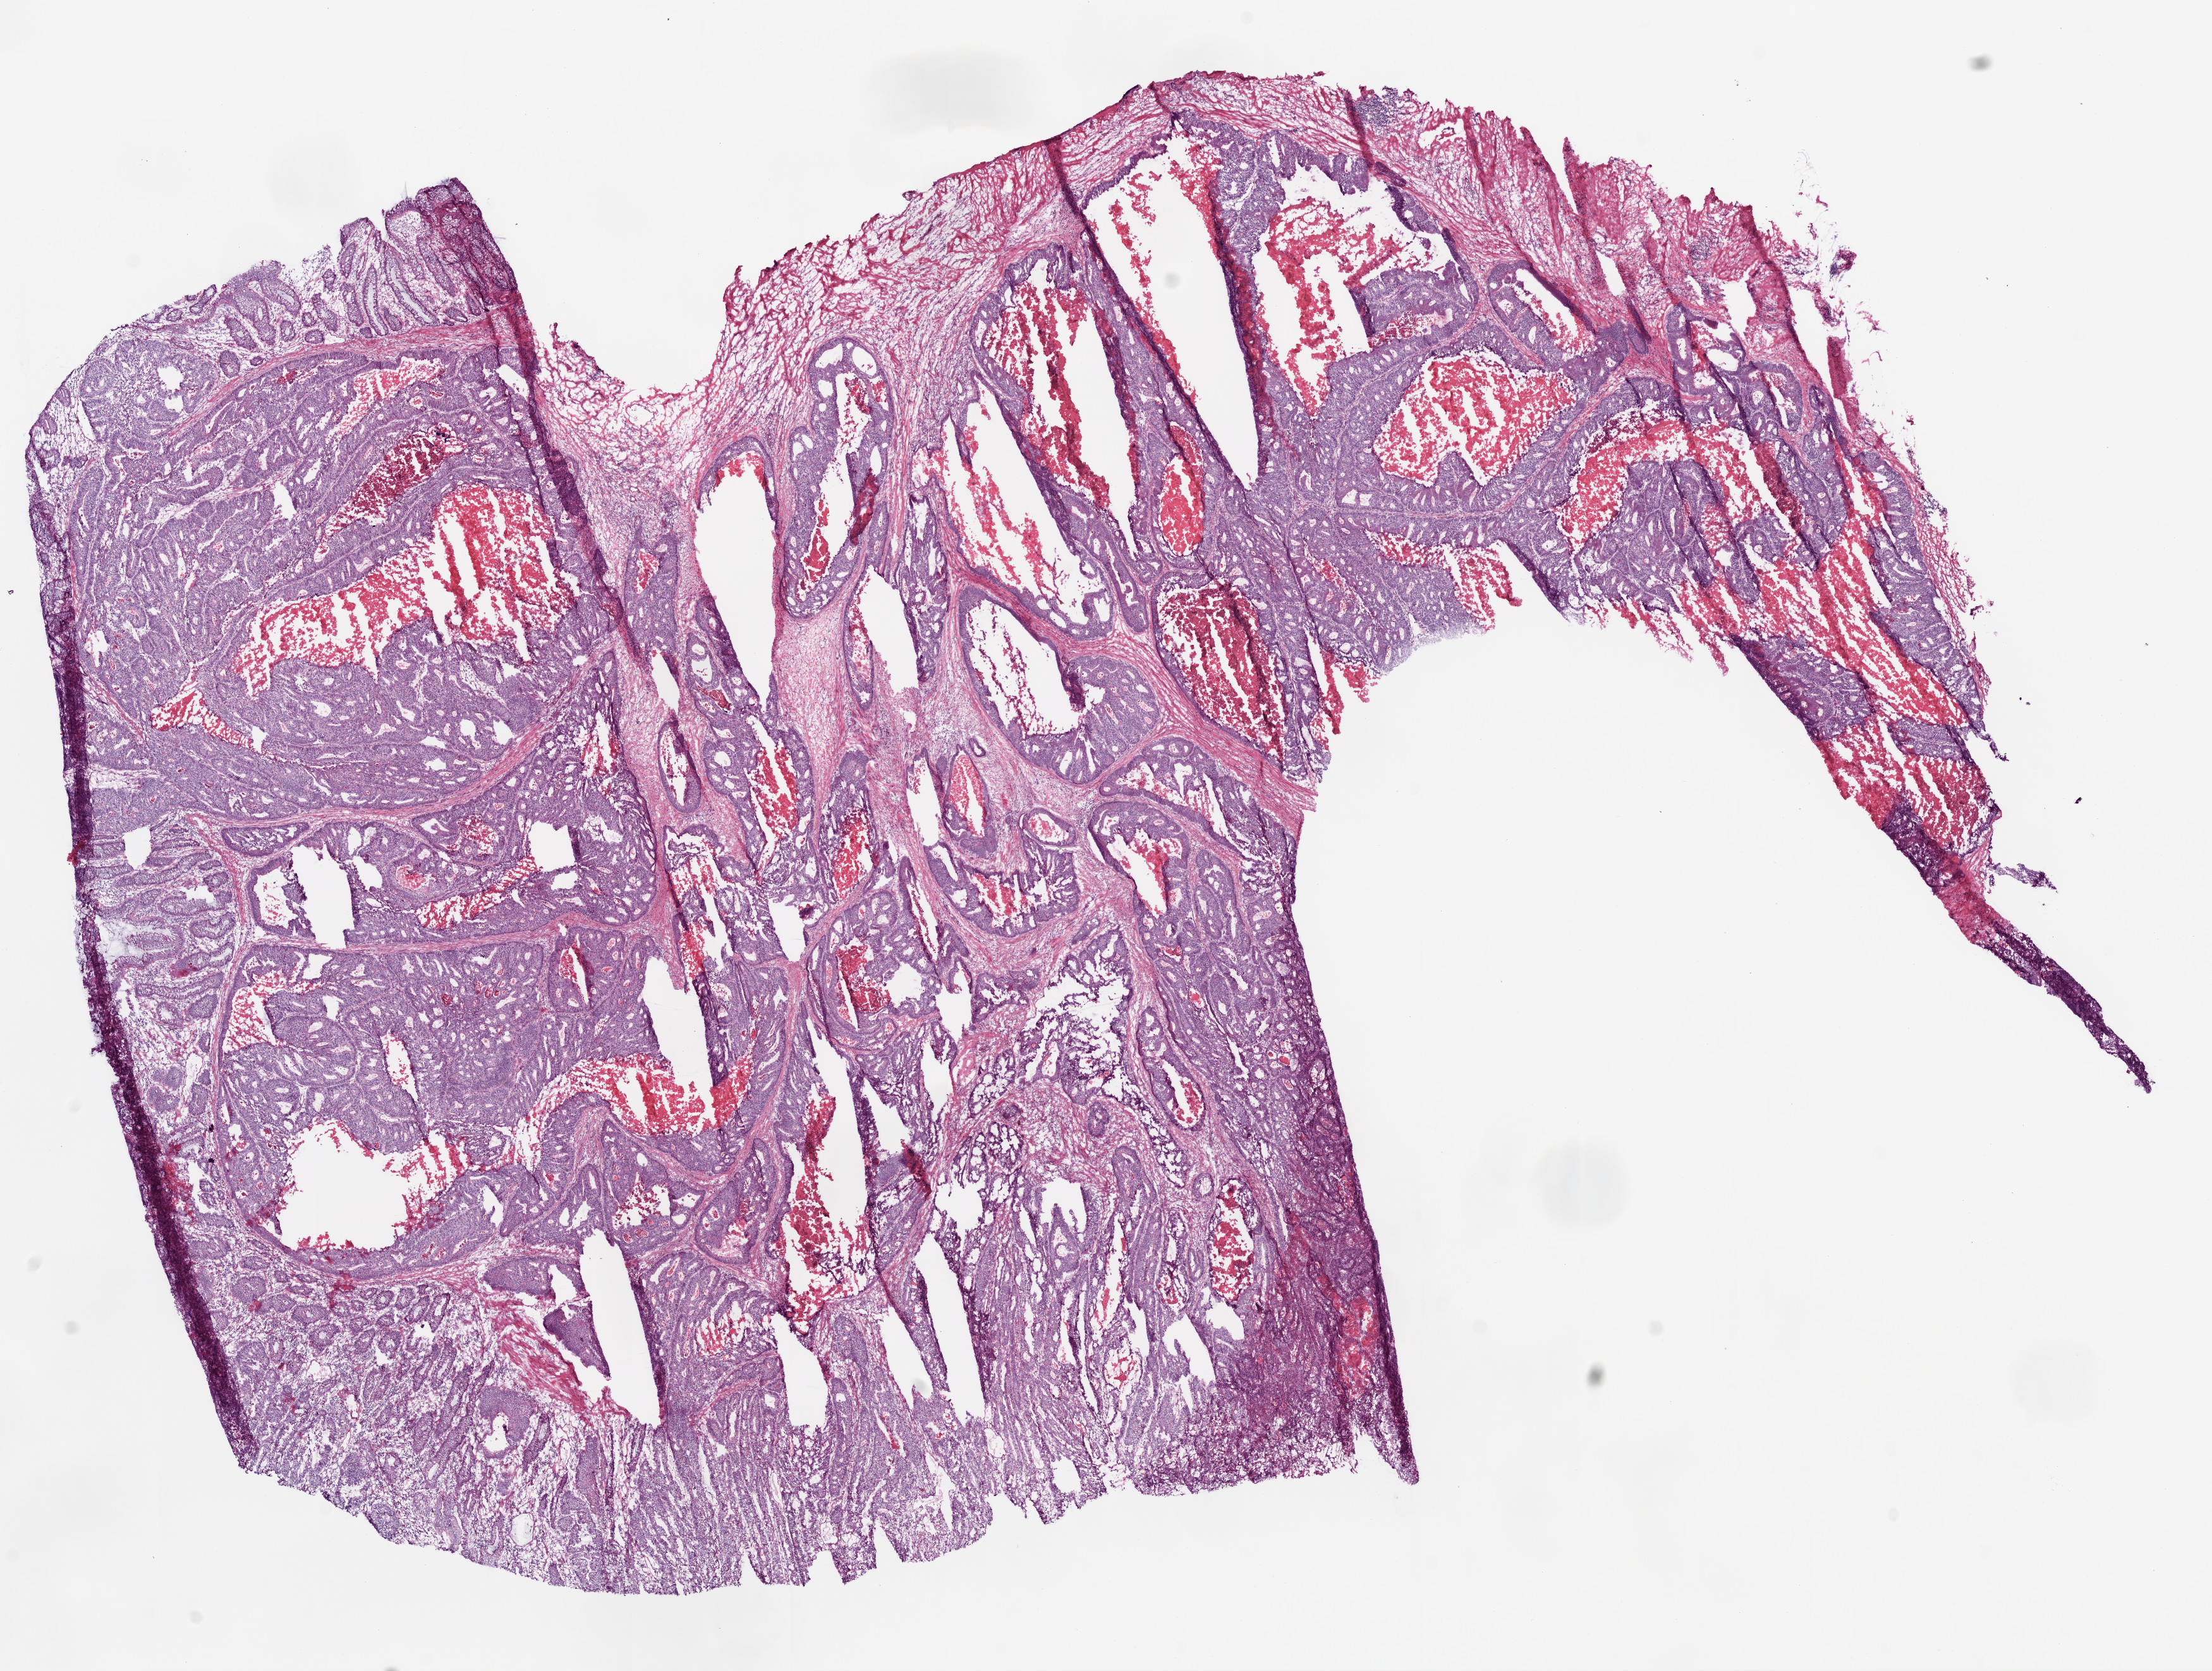
H&E-stained whole-slide image, low-resolution overview of the scanned area, about 14.0 x 10.6 mm; frozen section; sample: primary tumour, rectum. Female patient. Slide review estimates, as recorded: tumour cells 67%, tumour nuclei 75%, normal cells 5%, stromal cells 10%, necrosis 18%.
AJCC pathologic stage: II (5th edition). Lymph nodes positive (case pathology): 0 of 18 examined. Histologic diagnosis: Adenocarcinoma, NOS.